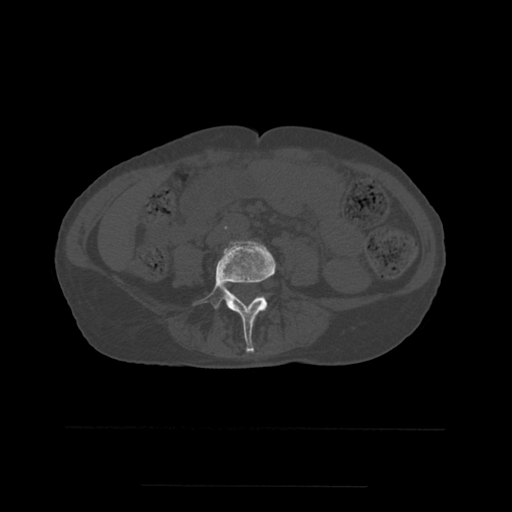
CT including the spine, one axial slice. Slice 165 of 544 in the series (ordered by position). Bone window (W 1800 / L 400 HU). 512 × 512 image matrix. Patient age 58 years. From the clinical record (not read from this slice): primary cancer: lung.
Structures marked on this image (semi-automatically segmented with operator editing):
- L4 vertebra: bounding box <195,241,276,353> (left, top, right, bottom; pixels)